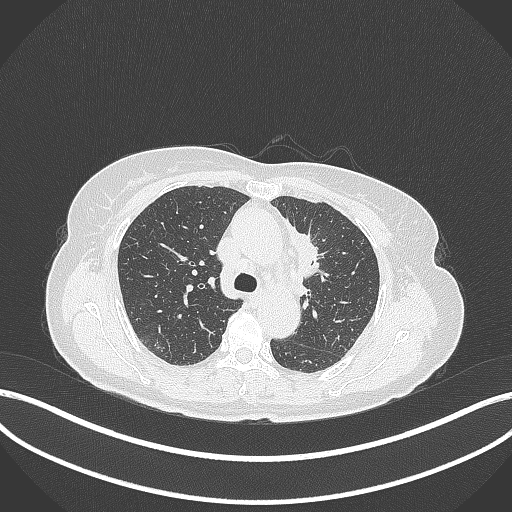
Chest CT, one axial slice; slice 230 of 369 in the series (ordered by position); reconstruction kernel B70f; lung window (W 1500 / L -600 HU); 1 mm slice thickness; 512 × 512 image matrix. Patient: female, 65 years. Case-level facts recorded for this patient, not image findings: clinical TNM (as recorded): T2a N0 M0; histopathological grade: G2-3.
Structures marked on this image (rectangle marked by the reading radiologist):
- lung tumour (recorded histology: adenocarcinoma): box from (x=281, y=219) to (x=324, y=279) px